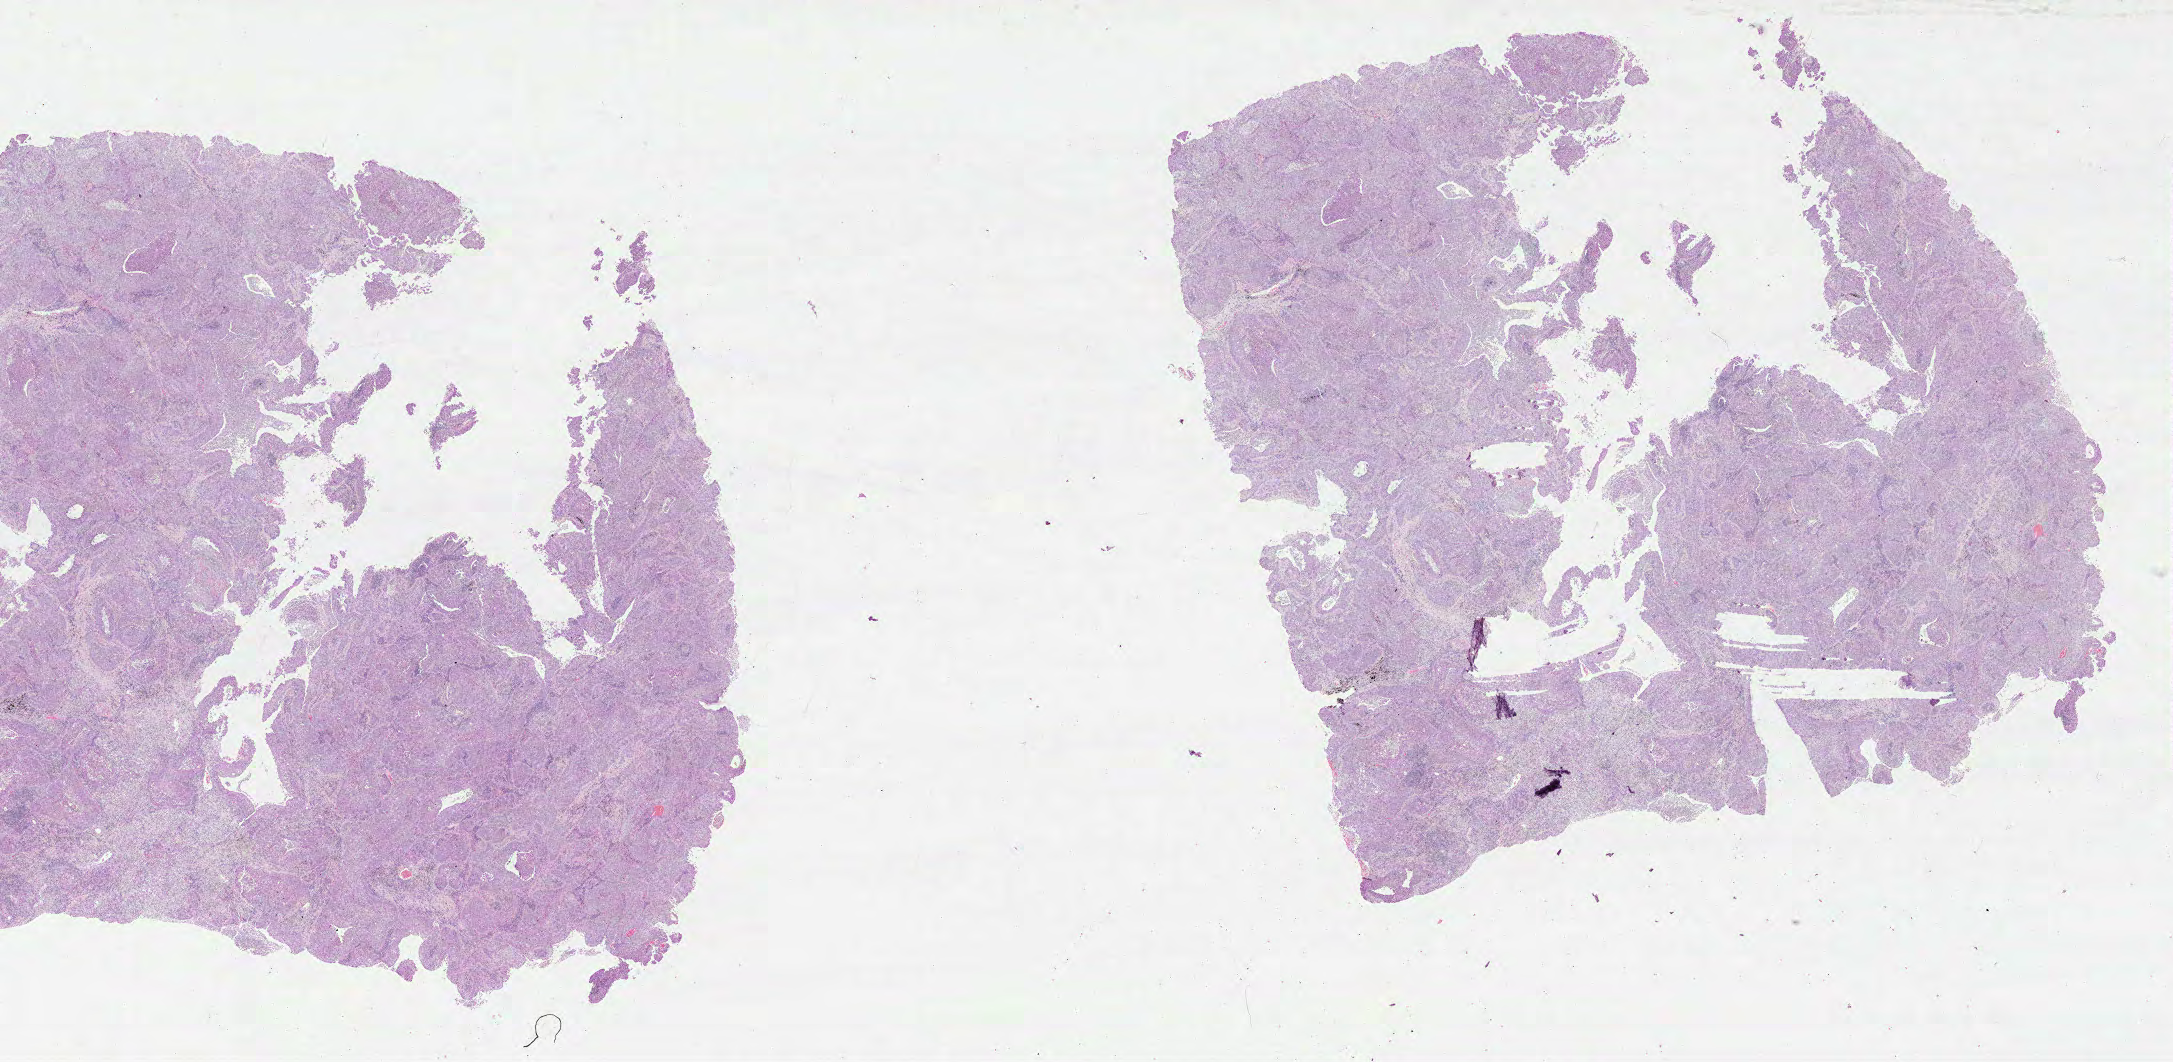
Digitized Hematoxylin and eosin (H&E) stained tissue section (whole slide) — shown as a low-resolution overview of the whole scanned area (about 35.1 x 17.1 mm, from a 40x scan), formalin-fixed paraffin-embedded (FFPE) diagnostic section, primary tumour sample from the lung. Patient: male, age at initial diagnosis 69 years.
• diagnosis: Squamous cell carcinoma, NOS (lower lobe, lung)
• AJCC pathologic stage: IB (6th edition)